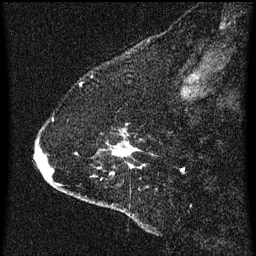
Breast MRI (dynamic contrast-enhanced), one sagittal slice. Position 13 of 60 along the scan axis. Dynamic contrast-enhanced series, image 2 of 3 at this slice position (ordered by acquisition). 1.5 T. TE 4.2 ms, TR 8 ms. 256 × 256 image matrix, field of view 180 × 180 mm. Female patient, age 47 years.
Annotated regions visible in this slice (semi-automatic segmentation, software-assisted and operator-edited):
- analysis volume of interest (the breast-tissue region the enhancement analysis was run in; not a lesion): bounding box (x1, y1, x2, y2) in pixels: (36, 118, 154, 213)
- tumour enhancement mask (voxels above the 70 % enhancement threshold inside the analysis volume of interest): (36, 150, 133, 175)